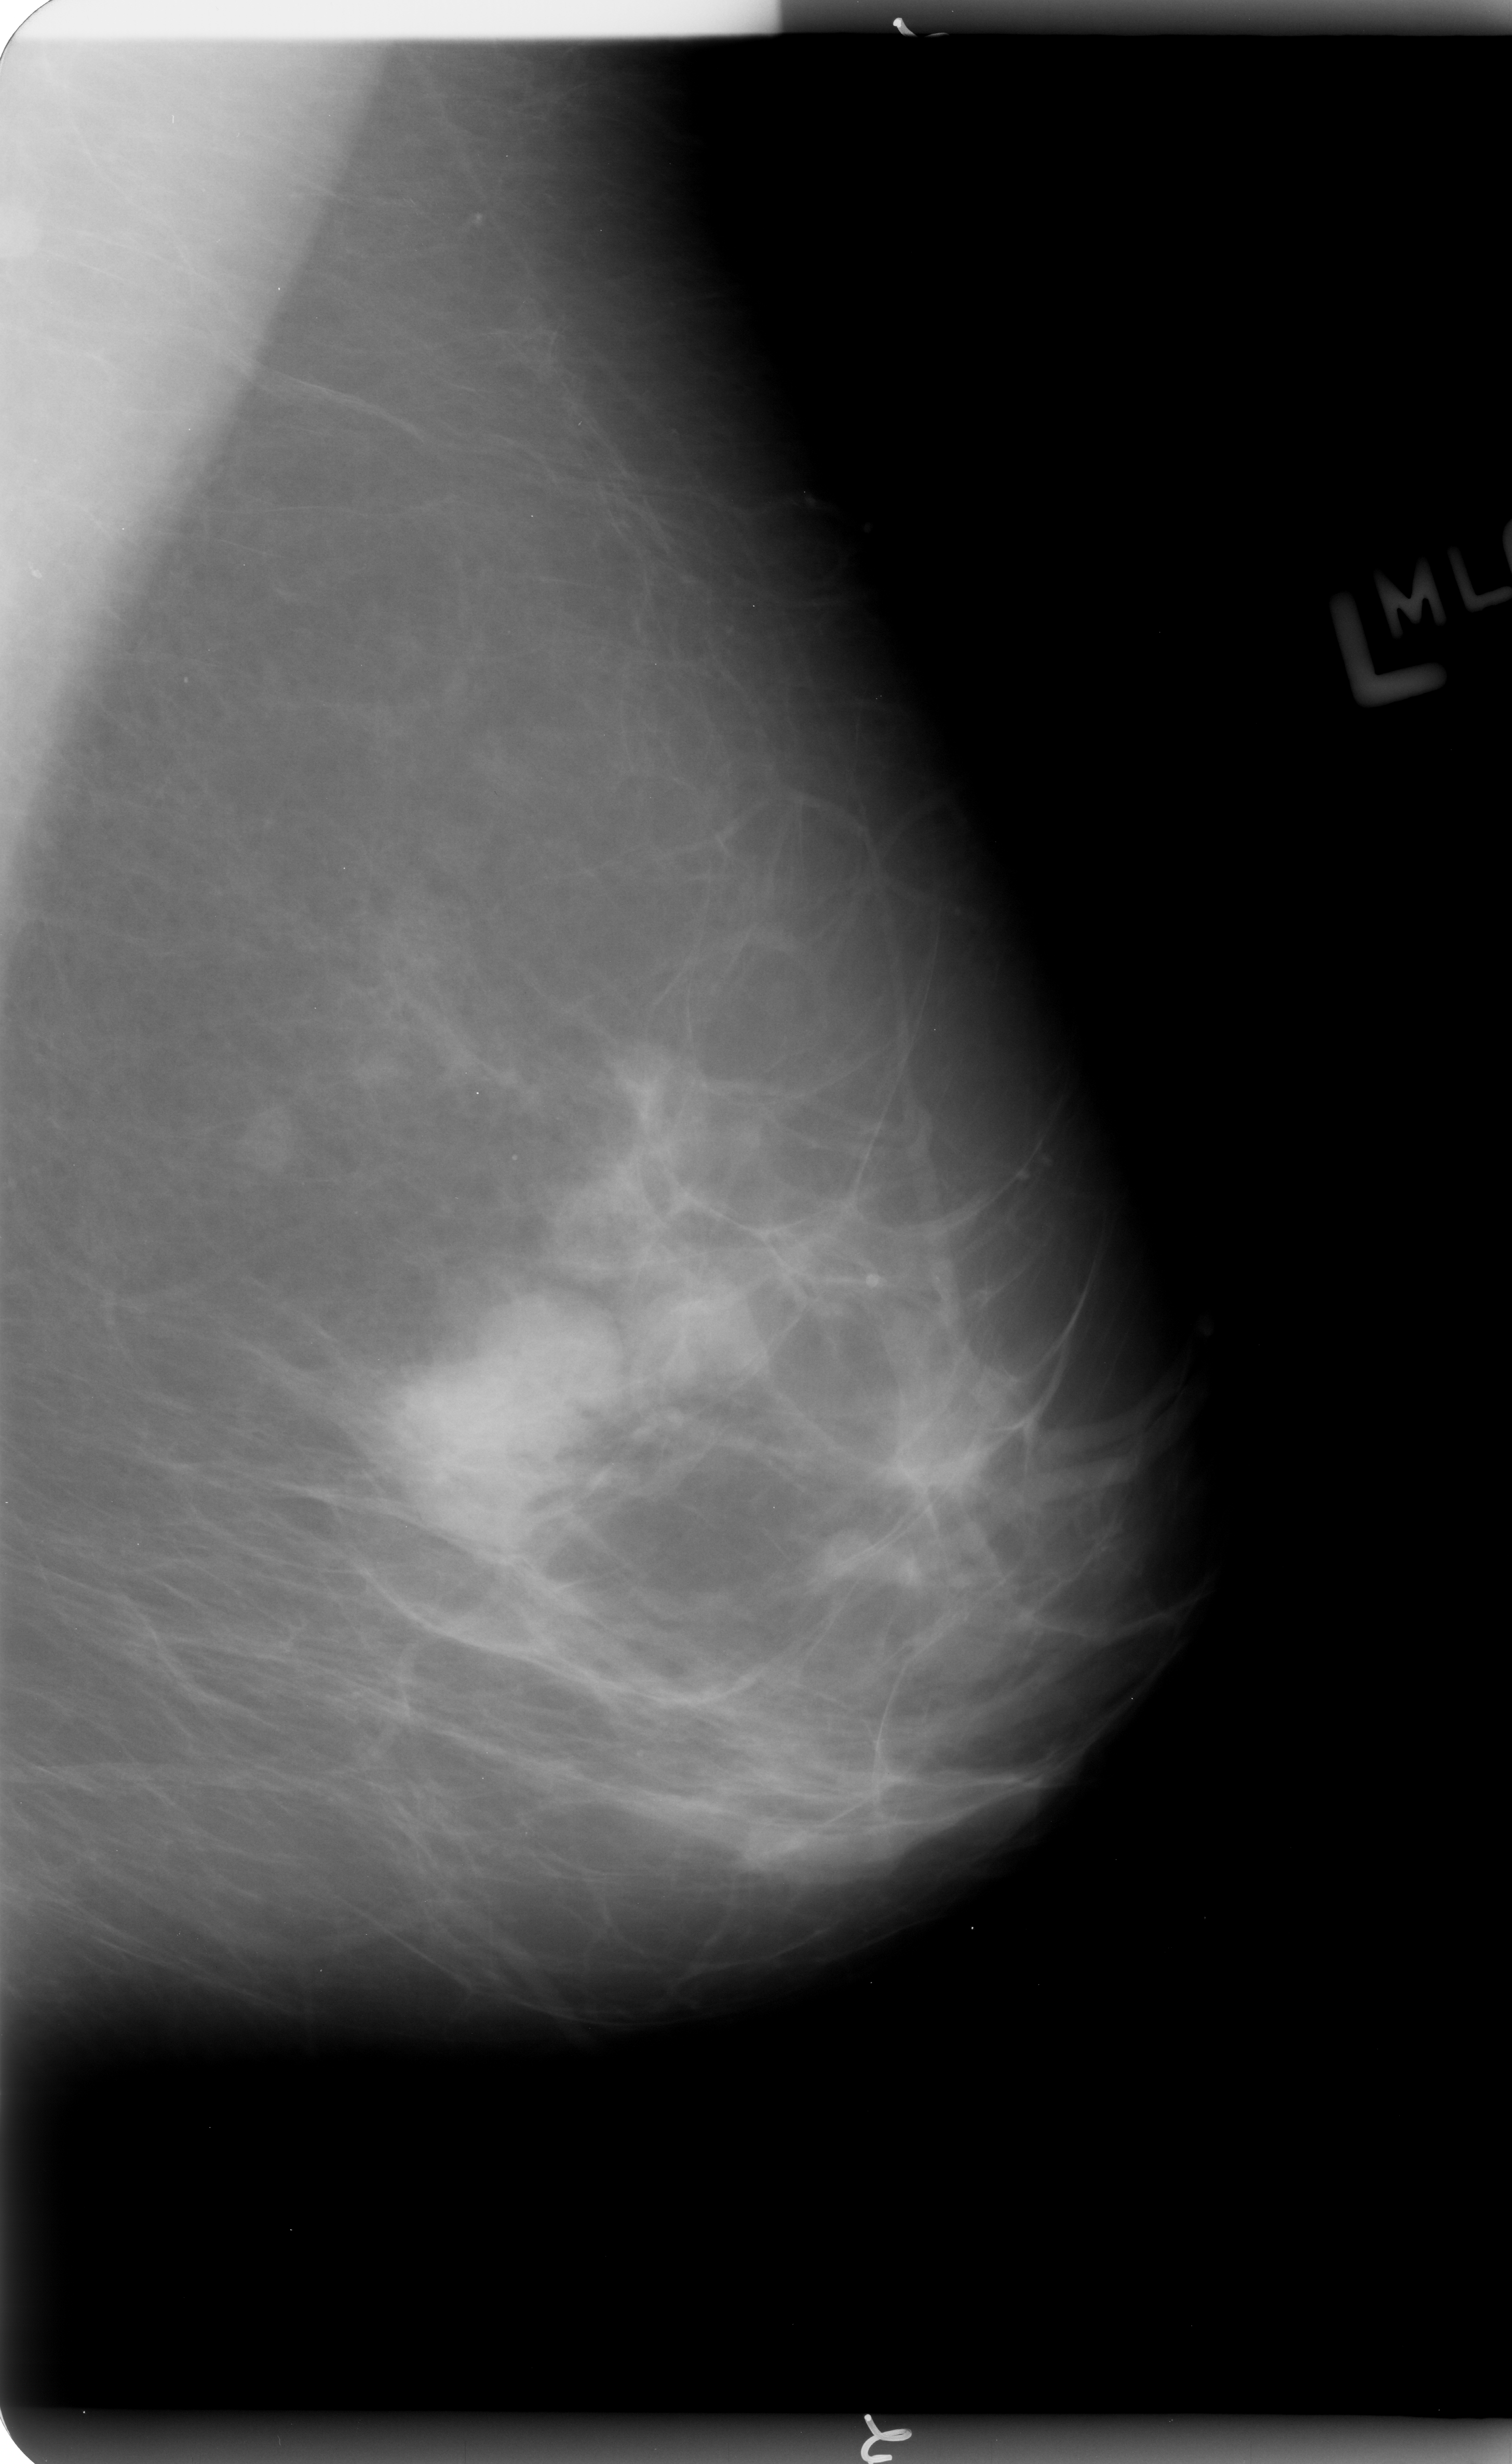
Digitized screen-film mammogram. Left breast. MLO view. BI-RADS breast density category 2 (scale 1–4). 1512 × 2464 image matrix.
Expert-marked regions of interest on this image (one box per marked abnormality):
- mass, shape lobulated, margins circumscribed / ill defined; BI-RADS assessment category 4; subtlety rating 3 on a 1 (subtle) to 5 (obvious) scale; pathology result (as recorded, not read from the image): benign: bounding box (x1, y1, x2, y2) in pixels: (388, 1332, 556, 1499)